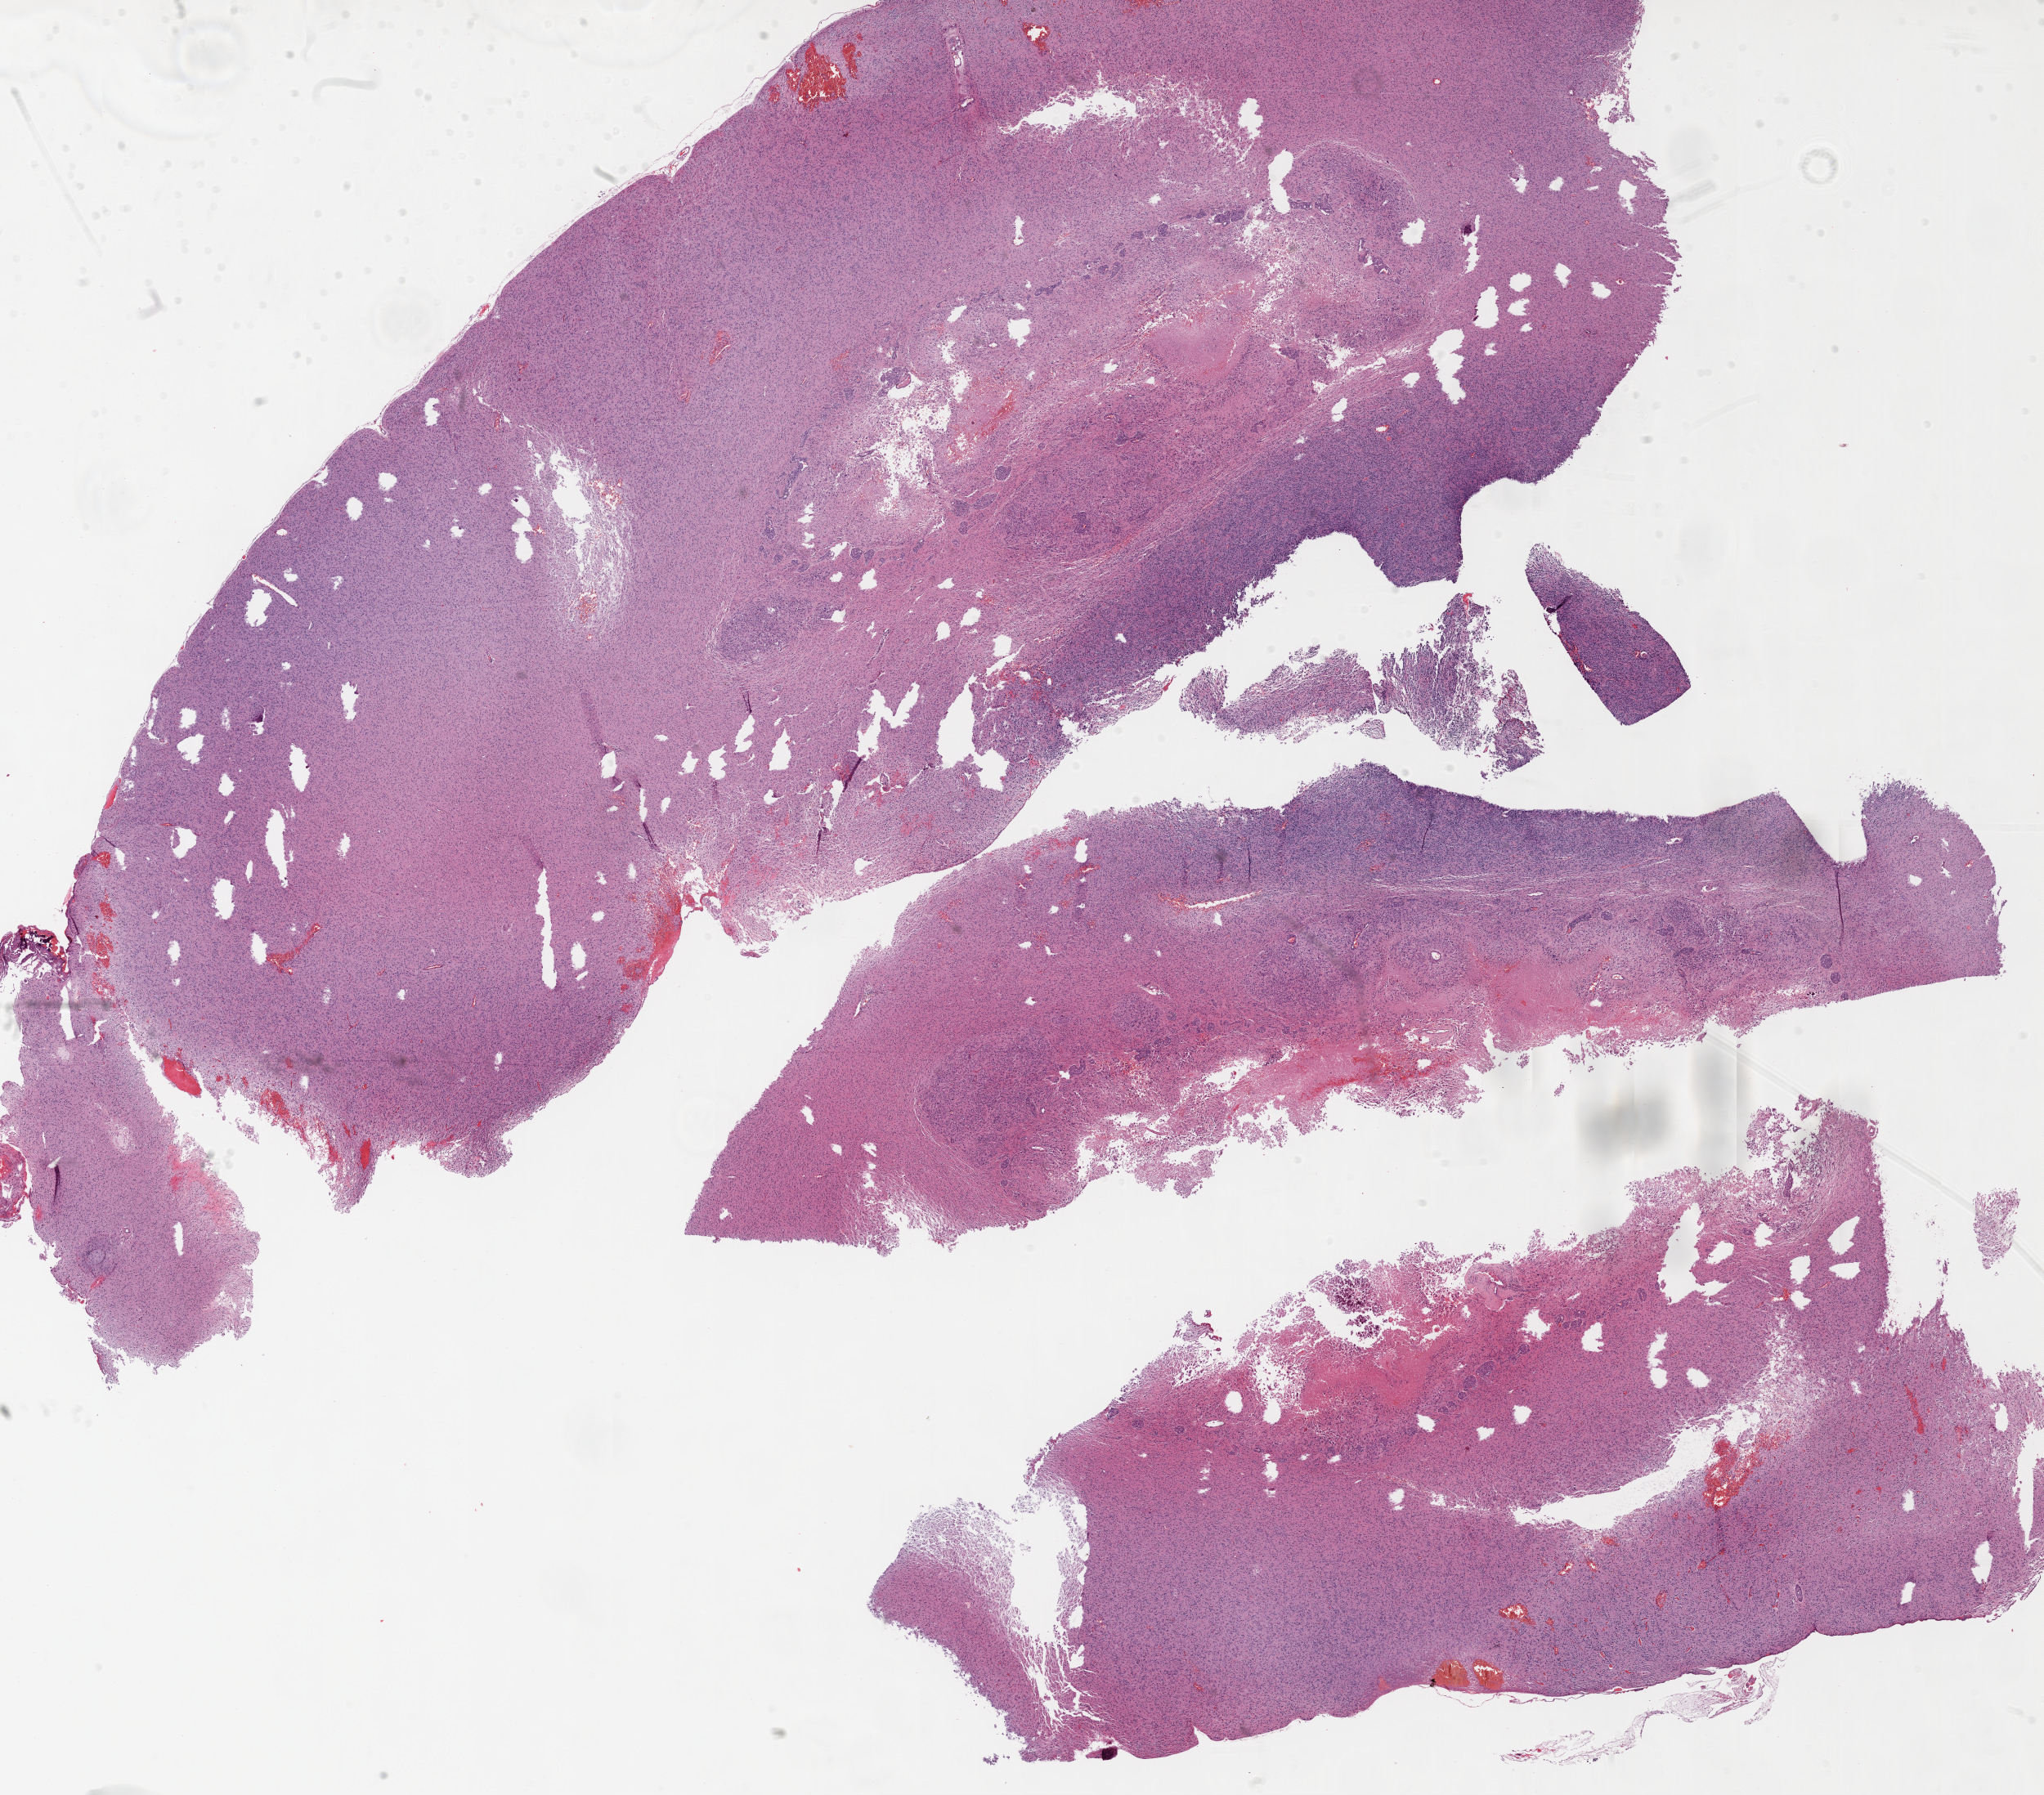
Whole-slide histology image, H&E-stained — low-resolution overview of the scanned area, about 20.1 x 17.6 mm (acquisition: 20x scan); FFPE section; primary tumour sample from the brain. Female patient; age at initial diagnosis 63 years.
Pathologic diagnosis: Glioblastoma.